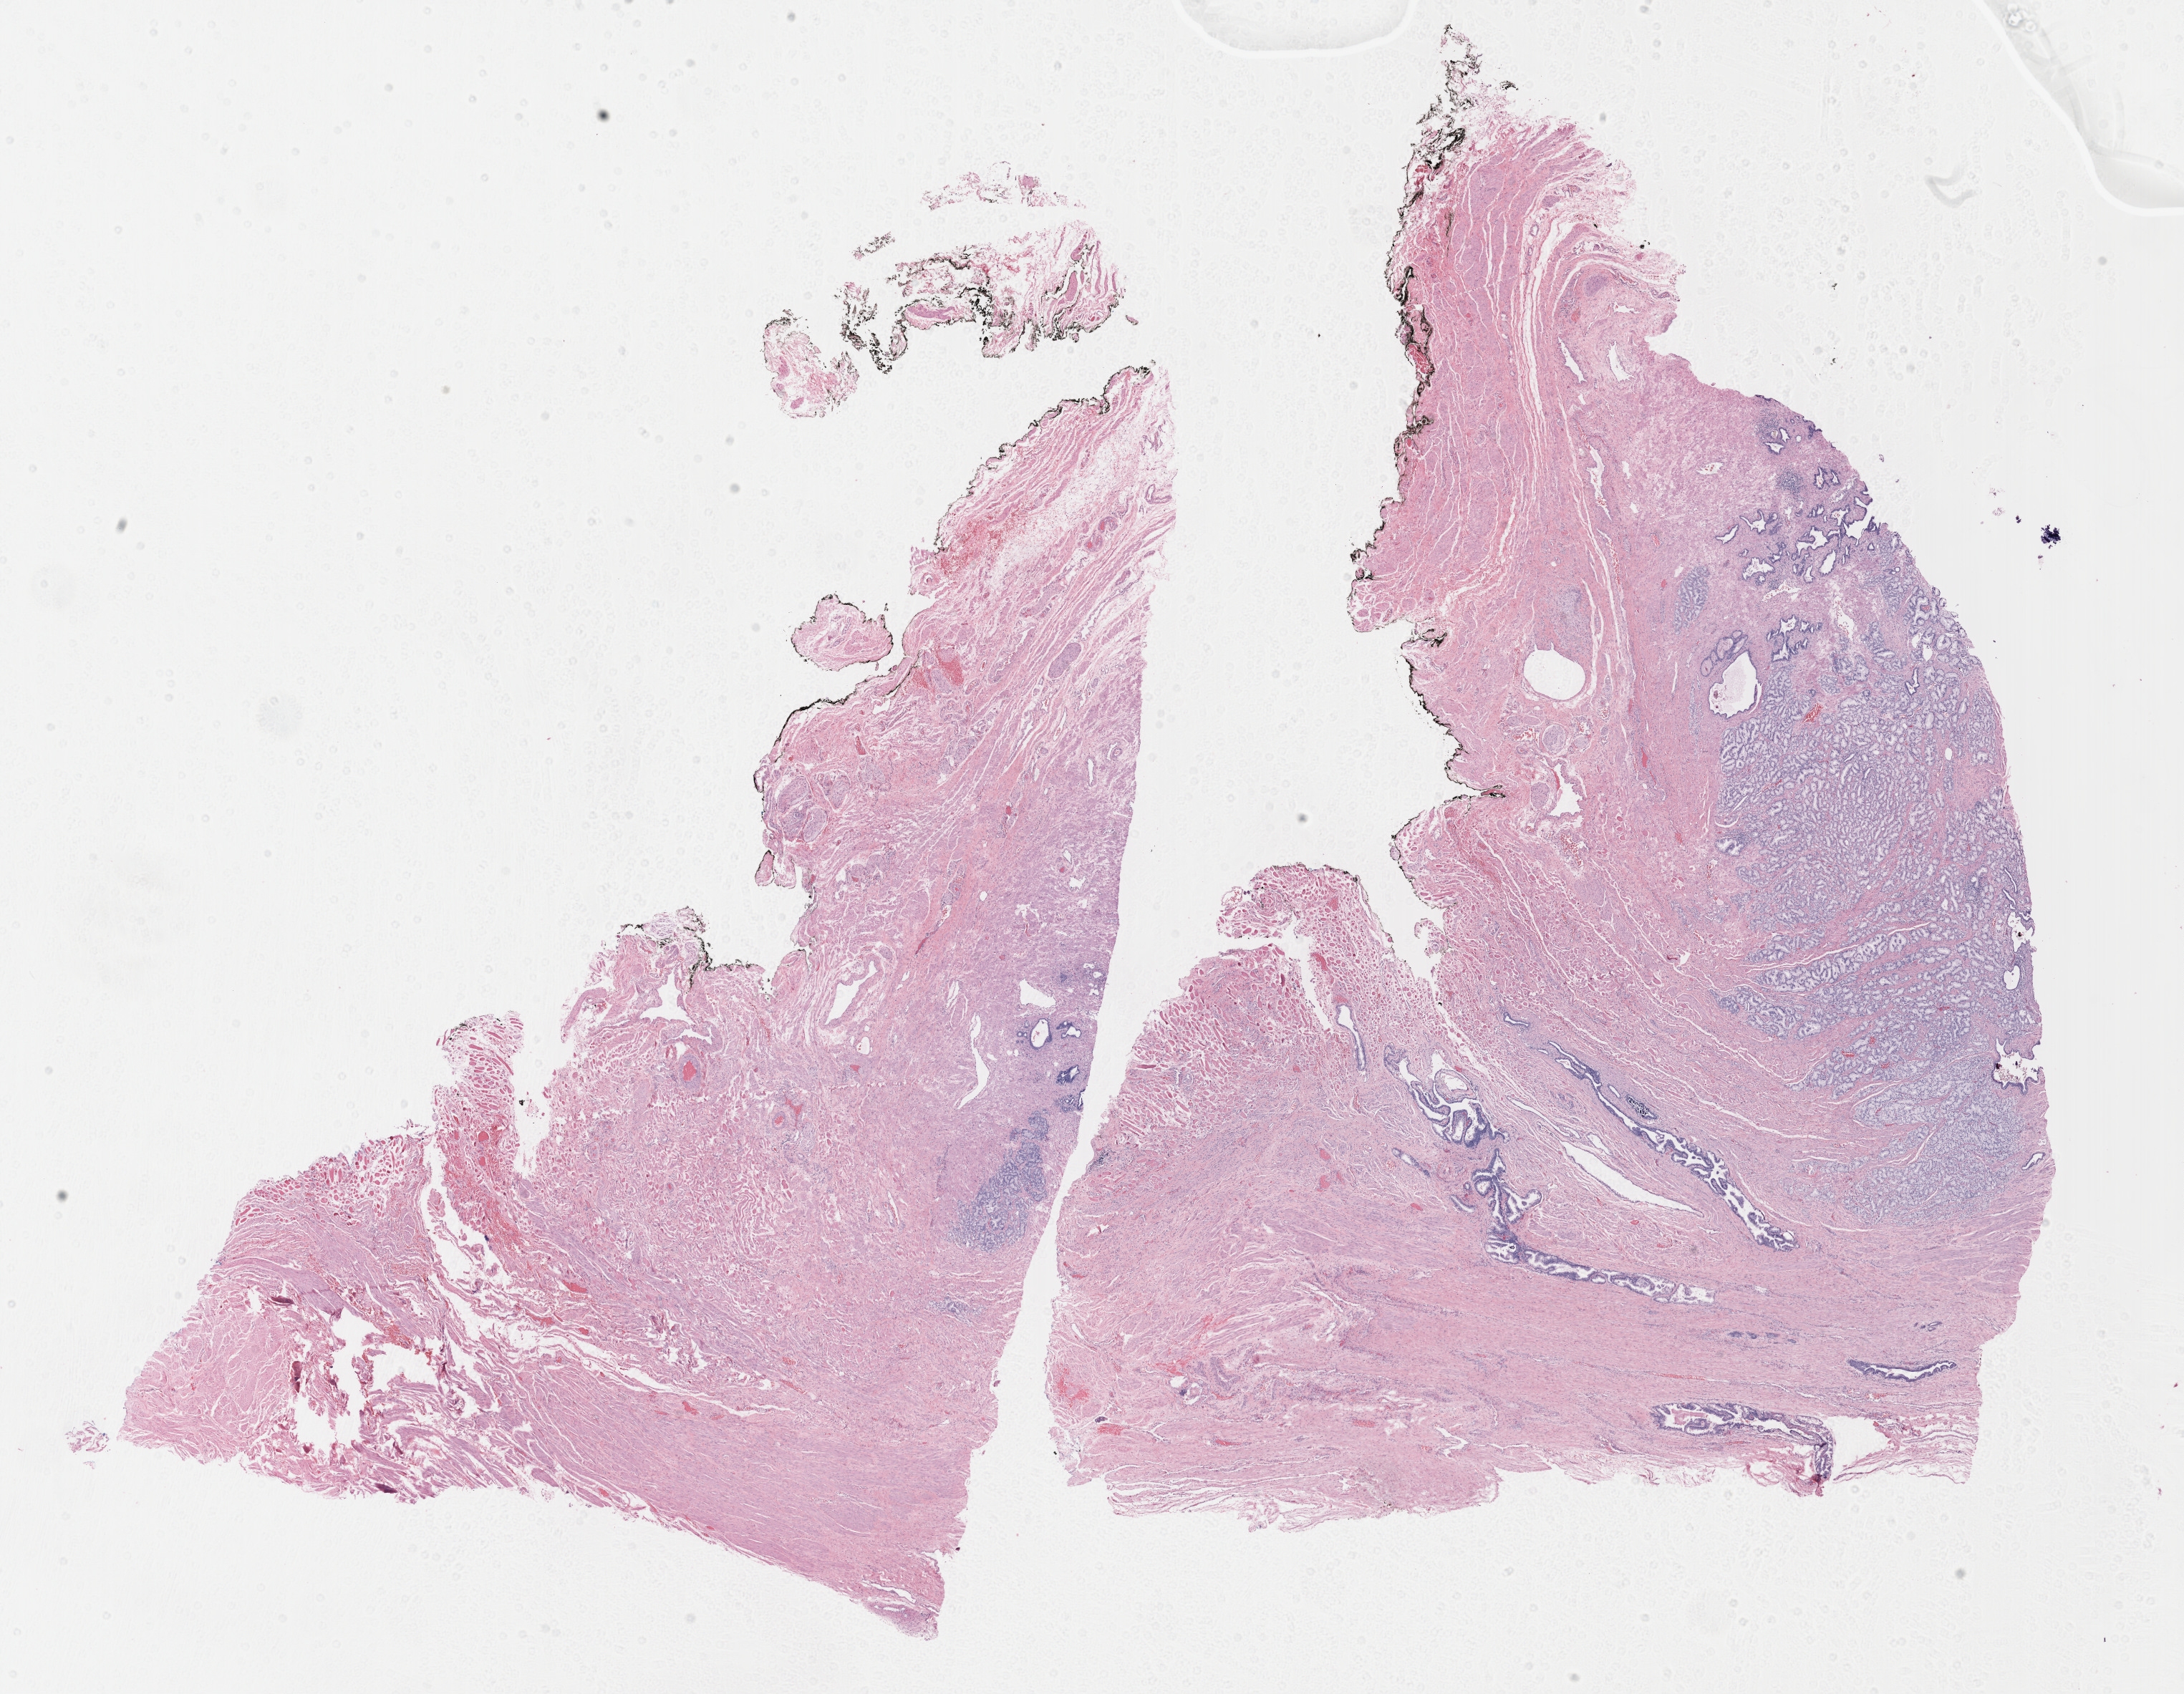
Hematoxylin and eosin (H&E) stained whole-slide image — whole scanned area (about 24.7 x 19.1 mm, slide scanned at 40x) shown as a low-resolution overview; formalin-fixed paraffin-embedded (FFPE) diagnostic section; primary tumour sample from the prostate. Patient: male, age at initial diagnosis 70 years. Gleason score: 8 (4+4).
Histologic diagnosis: Adenocarcinoma, NOS (prostate gland).